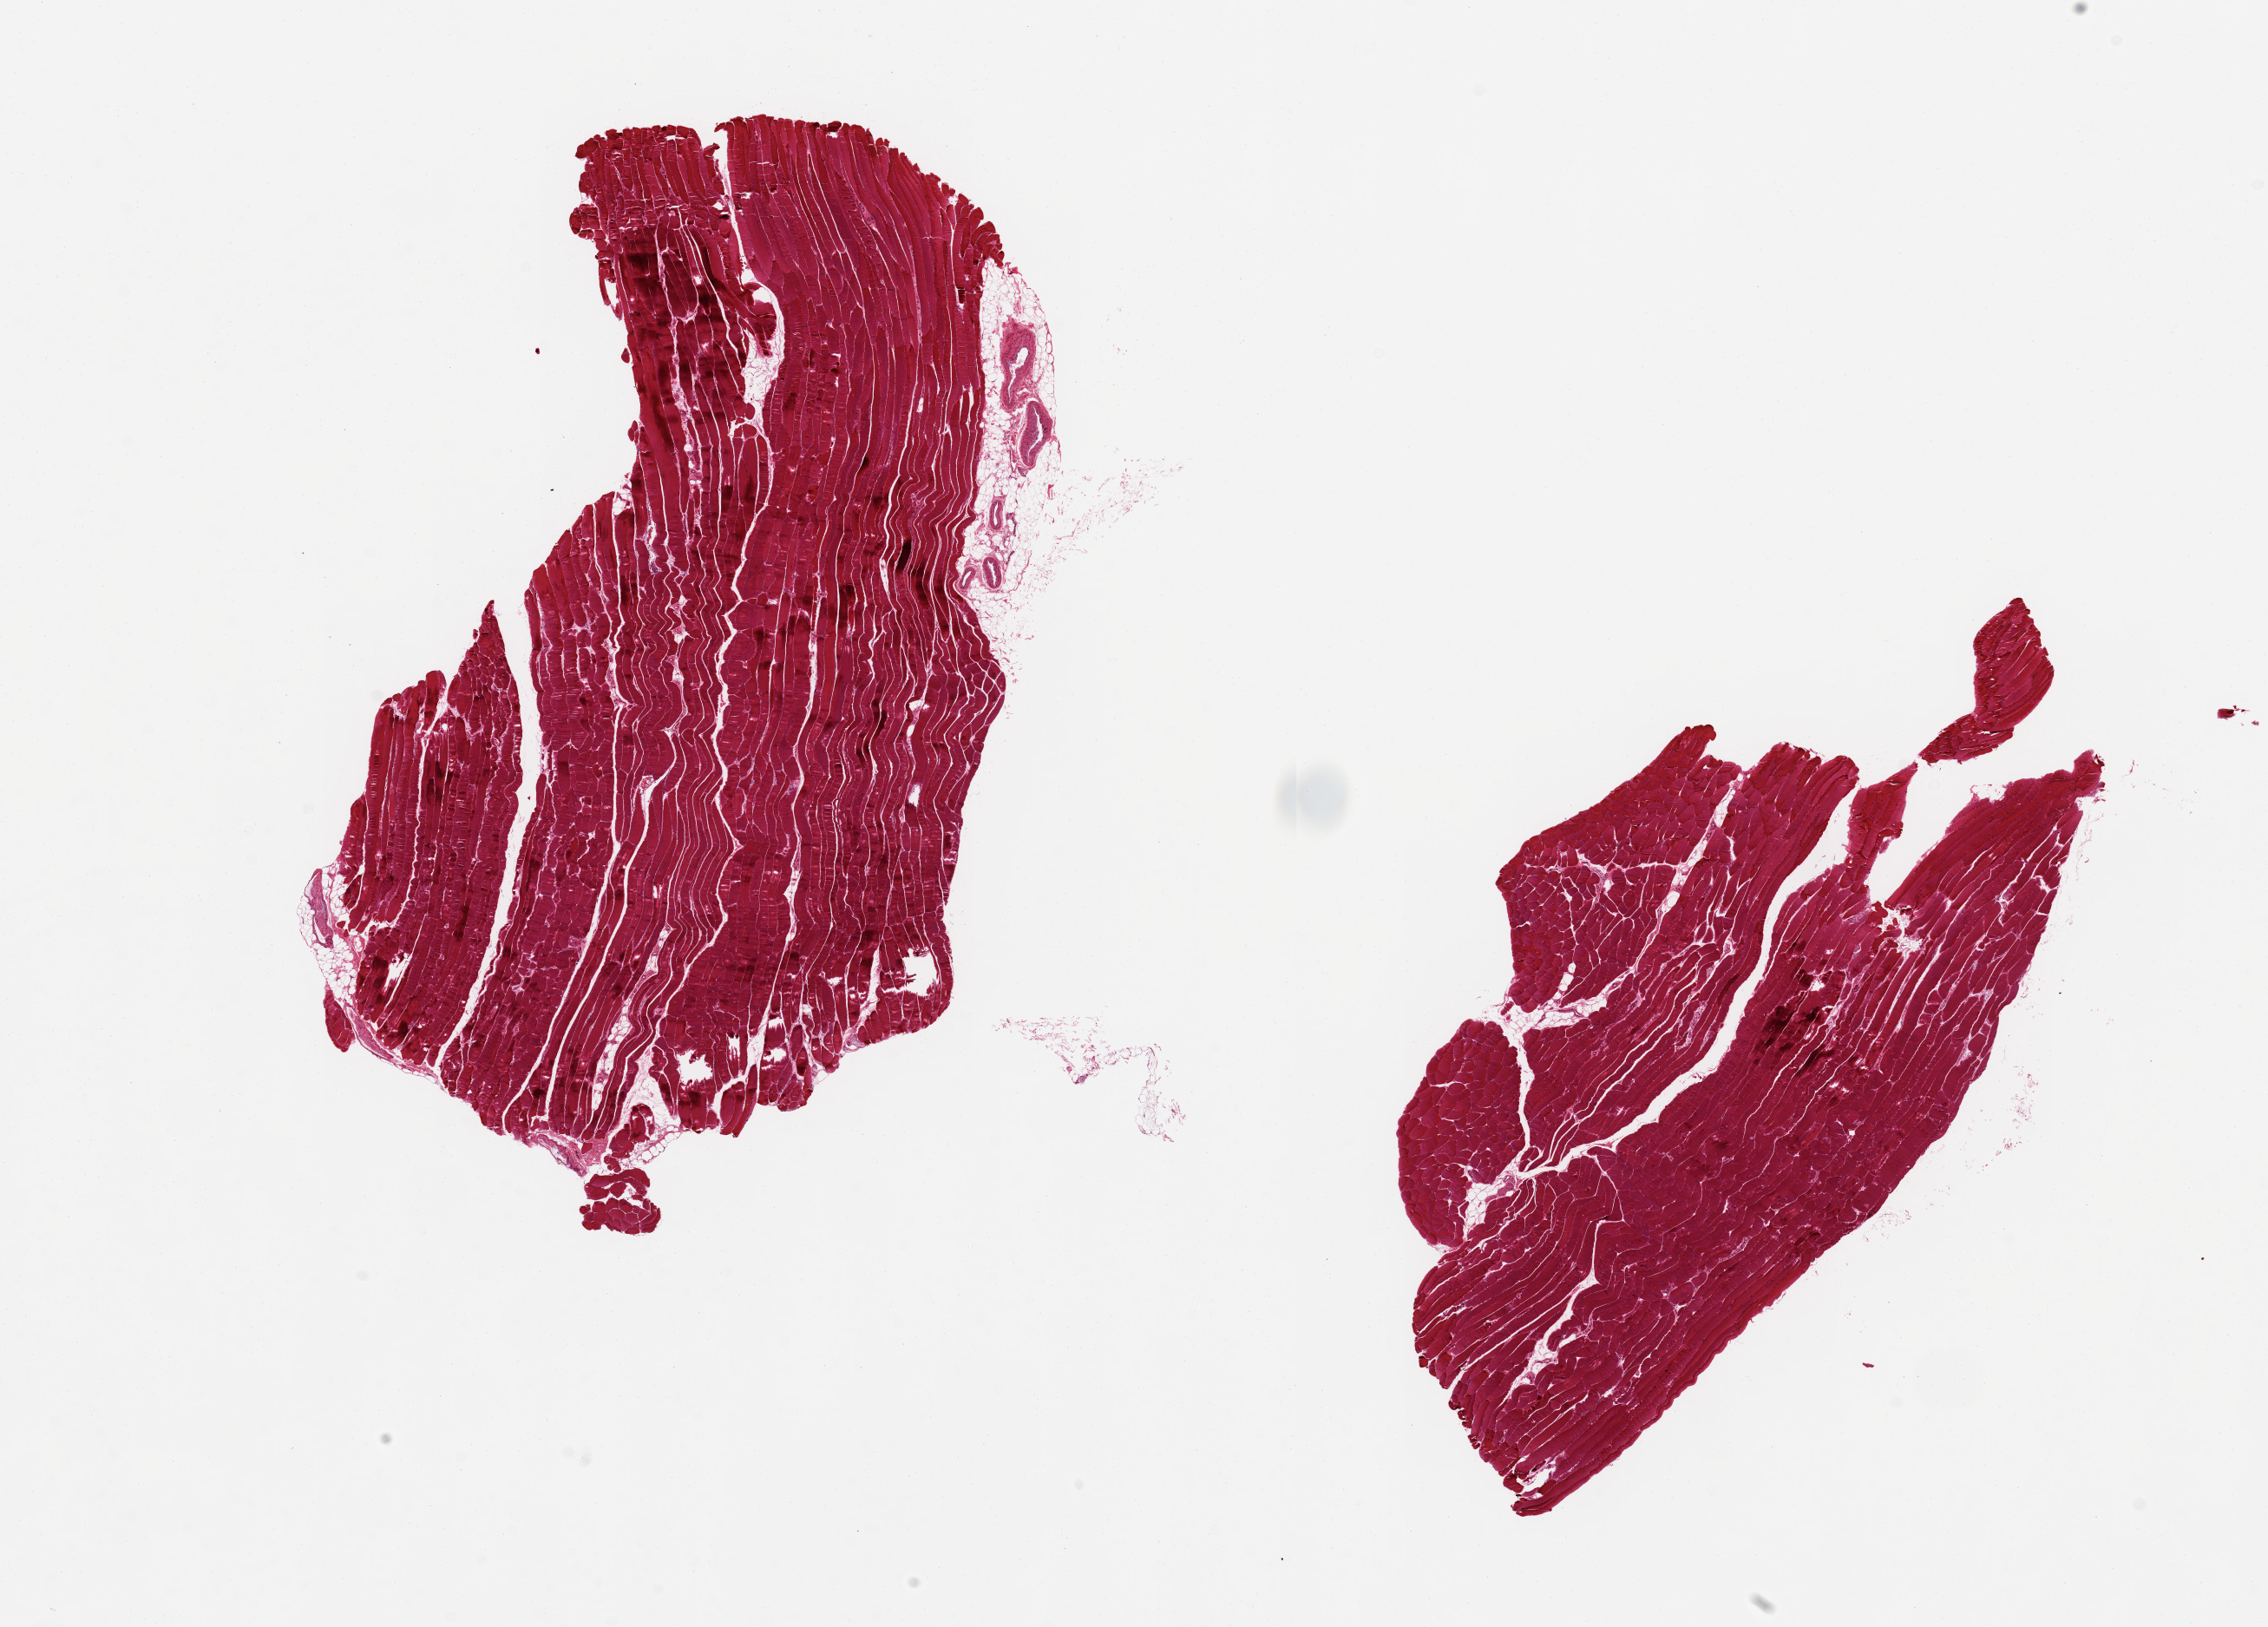
Digitized hematoxylin and eosin (H&E)-stained section — shown as a low-resolution overview of the whole scanned area (about 20.7 x 14.8 mm, acquisition: 20x scan), PAXgene-fixed, paraffin-embedded tissue, section of skeletal muscle (target tissue), tissue donor sample. Donor sex: male.
Review note (as recorded): 2 aliquots, ~8.5x5mm. Minimal interstitial fat.